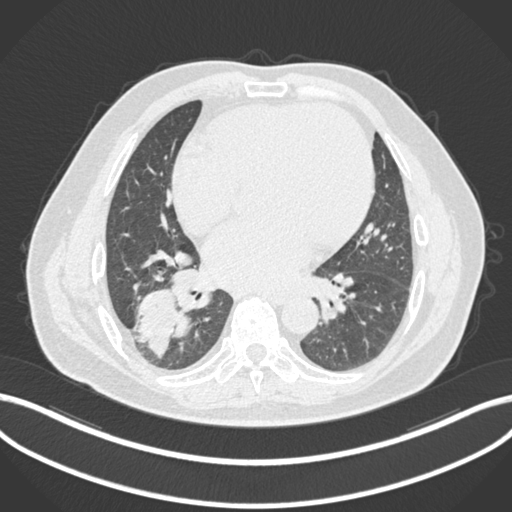
Chest CT, one axial slice. Slice 75 of 200 in the series (ordered by position). Reconstruction kernel B30f. Lung window (W 1500 / L -600 HU). 1 mm slice thickness. 512 × 512 image matrix, field of view 400 × 400 mm. Male patient, age 59 years.
Structures marked on this image (bounding box drawn by a radiologist):
- lung tumour (recorded histology: adenocarcinoma): bounding box (x1, y1, x2, y2) in pixels: (134, 286, 190, 360)